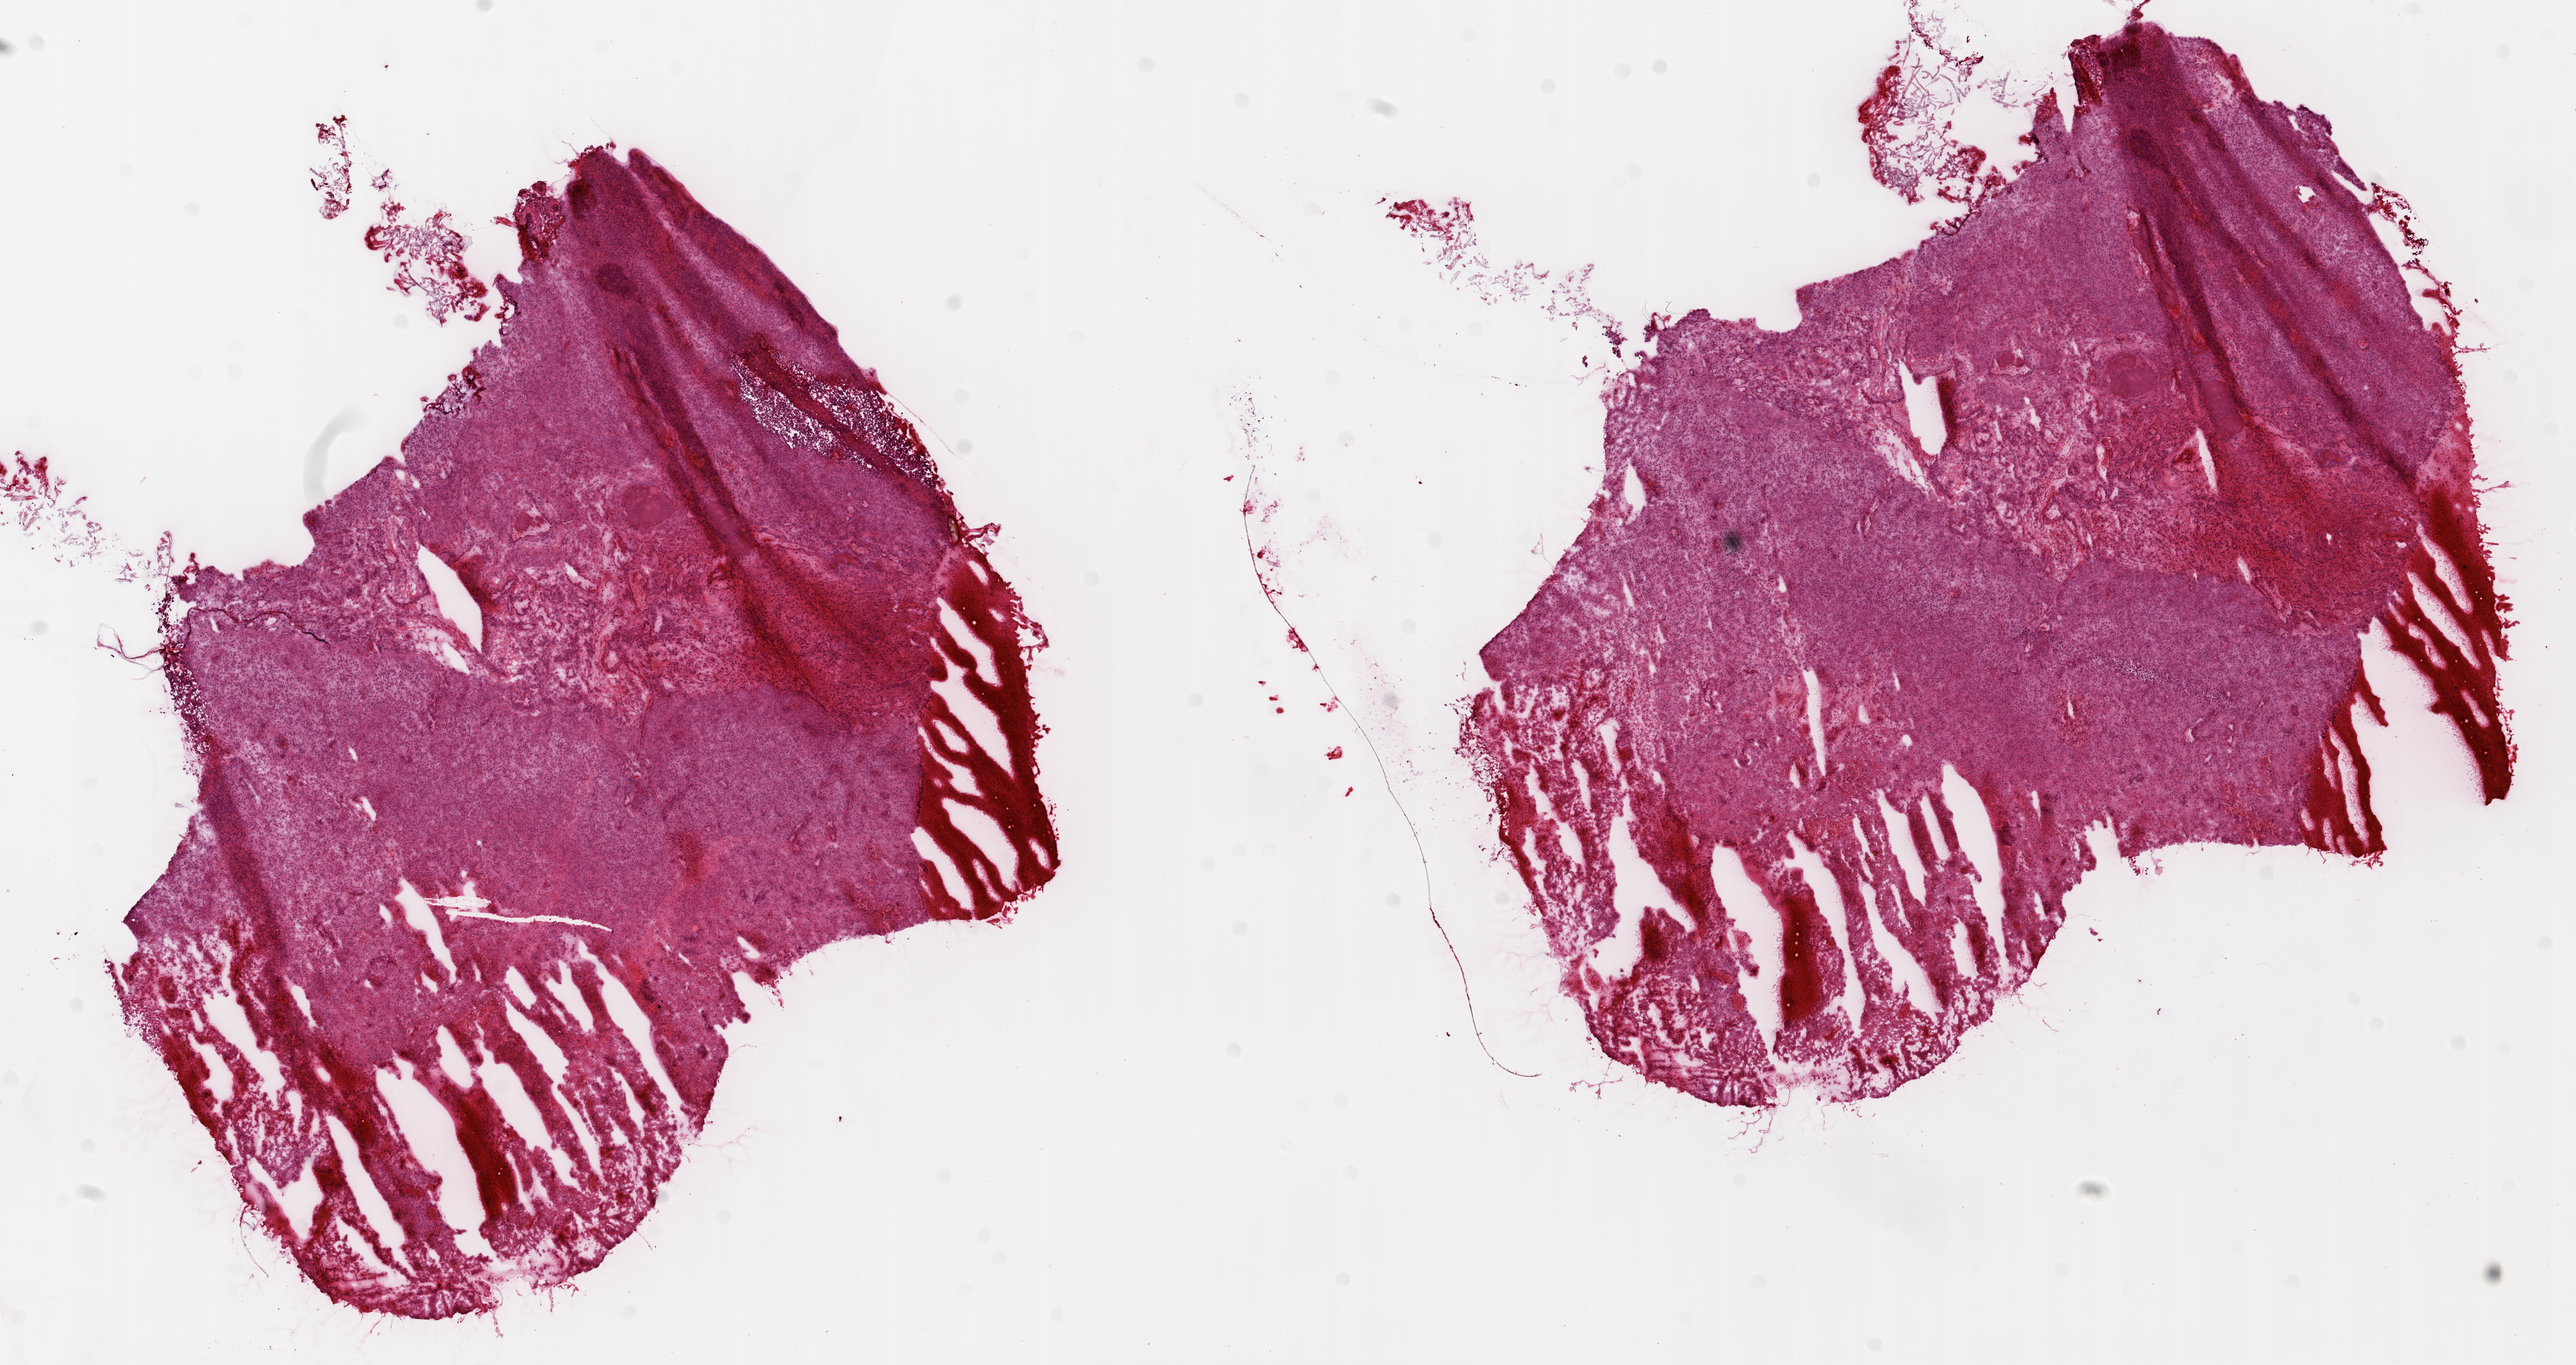
Whole-slide histology image, H&E-stained — low-resolution overview of the scanned area, about 16.4 x 8.7 mm (from a 20x scan); frozen section; primary tumour sample from the brain. Female, age 57 years at initial diagnosis.
Pathologic diagnosis: Glioblastoma.